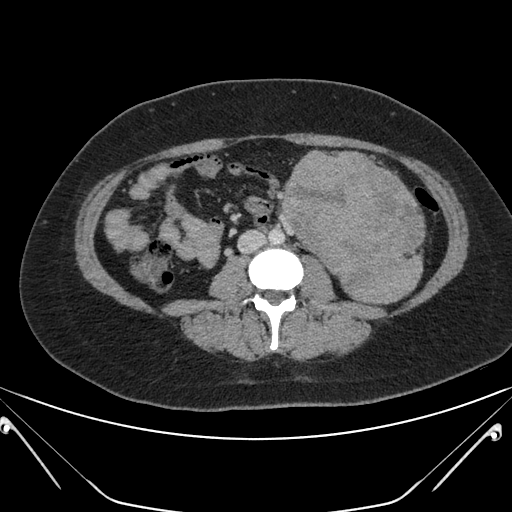
Contrast-enhanced abdominal CT, one axial slice. Position 88 of 168 along the scan axis. Intravenous contrast given. Soft-tissue window (W 400 / L 40 HU). 512 × 512 image matrix. Female patient, age 26 years. Case-level facts recorded for this patient, not image findings: diagnosis: adrenocortical carcinoma; tumour side: left adrenal; tumour size at pathology: 28 cm; Ki-67 index: 20 %; stage (as recorded): 2.
Outlined on this slice (semi-automatically segmented with operator editing):
- mass: bounding box [x1, y1, x2, y2] px = [284, 152, 422, 301]